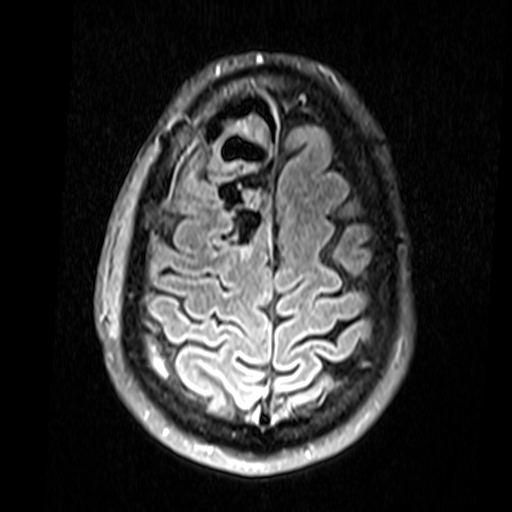
Brain MRI from a brain-tumour surgery series, one axial slice; slice 51 of 74 in the series (ordered by position); T2 FLAIR; 3.3 mm slice thickness; 512 × 512 image matrix. Case-level facts recorded for this patient, not image findings: histopathology: Glial fibroma.
Structures marked on this image (manually delineated by an expert):
- residual tumour: box from (x=214, y=160) to (x=261, y=258) px